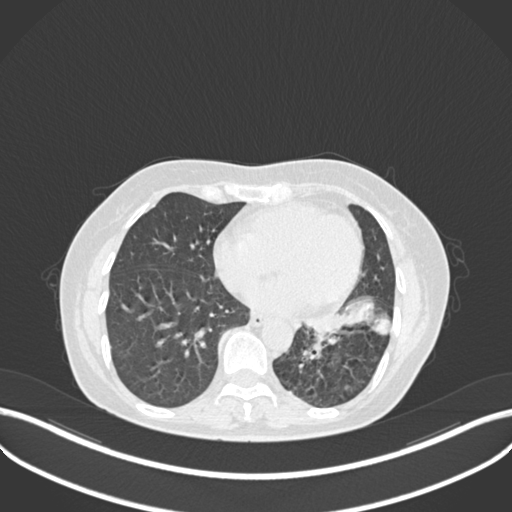
Chest CT, one axial slice; slice 98 of 270 in the series (ordered by position); lung window (W 1500 / L -600 HU); 512 × 512 image matrix, field of view 400 × 400 mm. Patient: female, 63 years. Case-level facts recorded for this patient, not image findings: clinical TNM (as recorded): T1b N0 M0.
Structures marked on this image (bounding box drawn by a radiologist):
- lung tumour (recorded histology: adenocarcinoma): bounding box <304,294,393,336> (left, top, right, bottom; pixels)